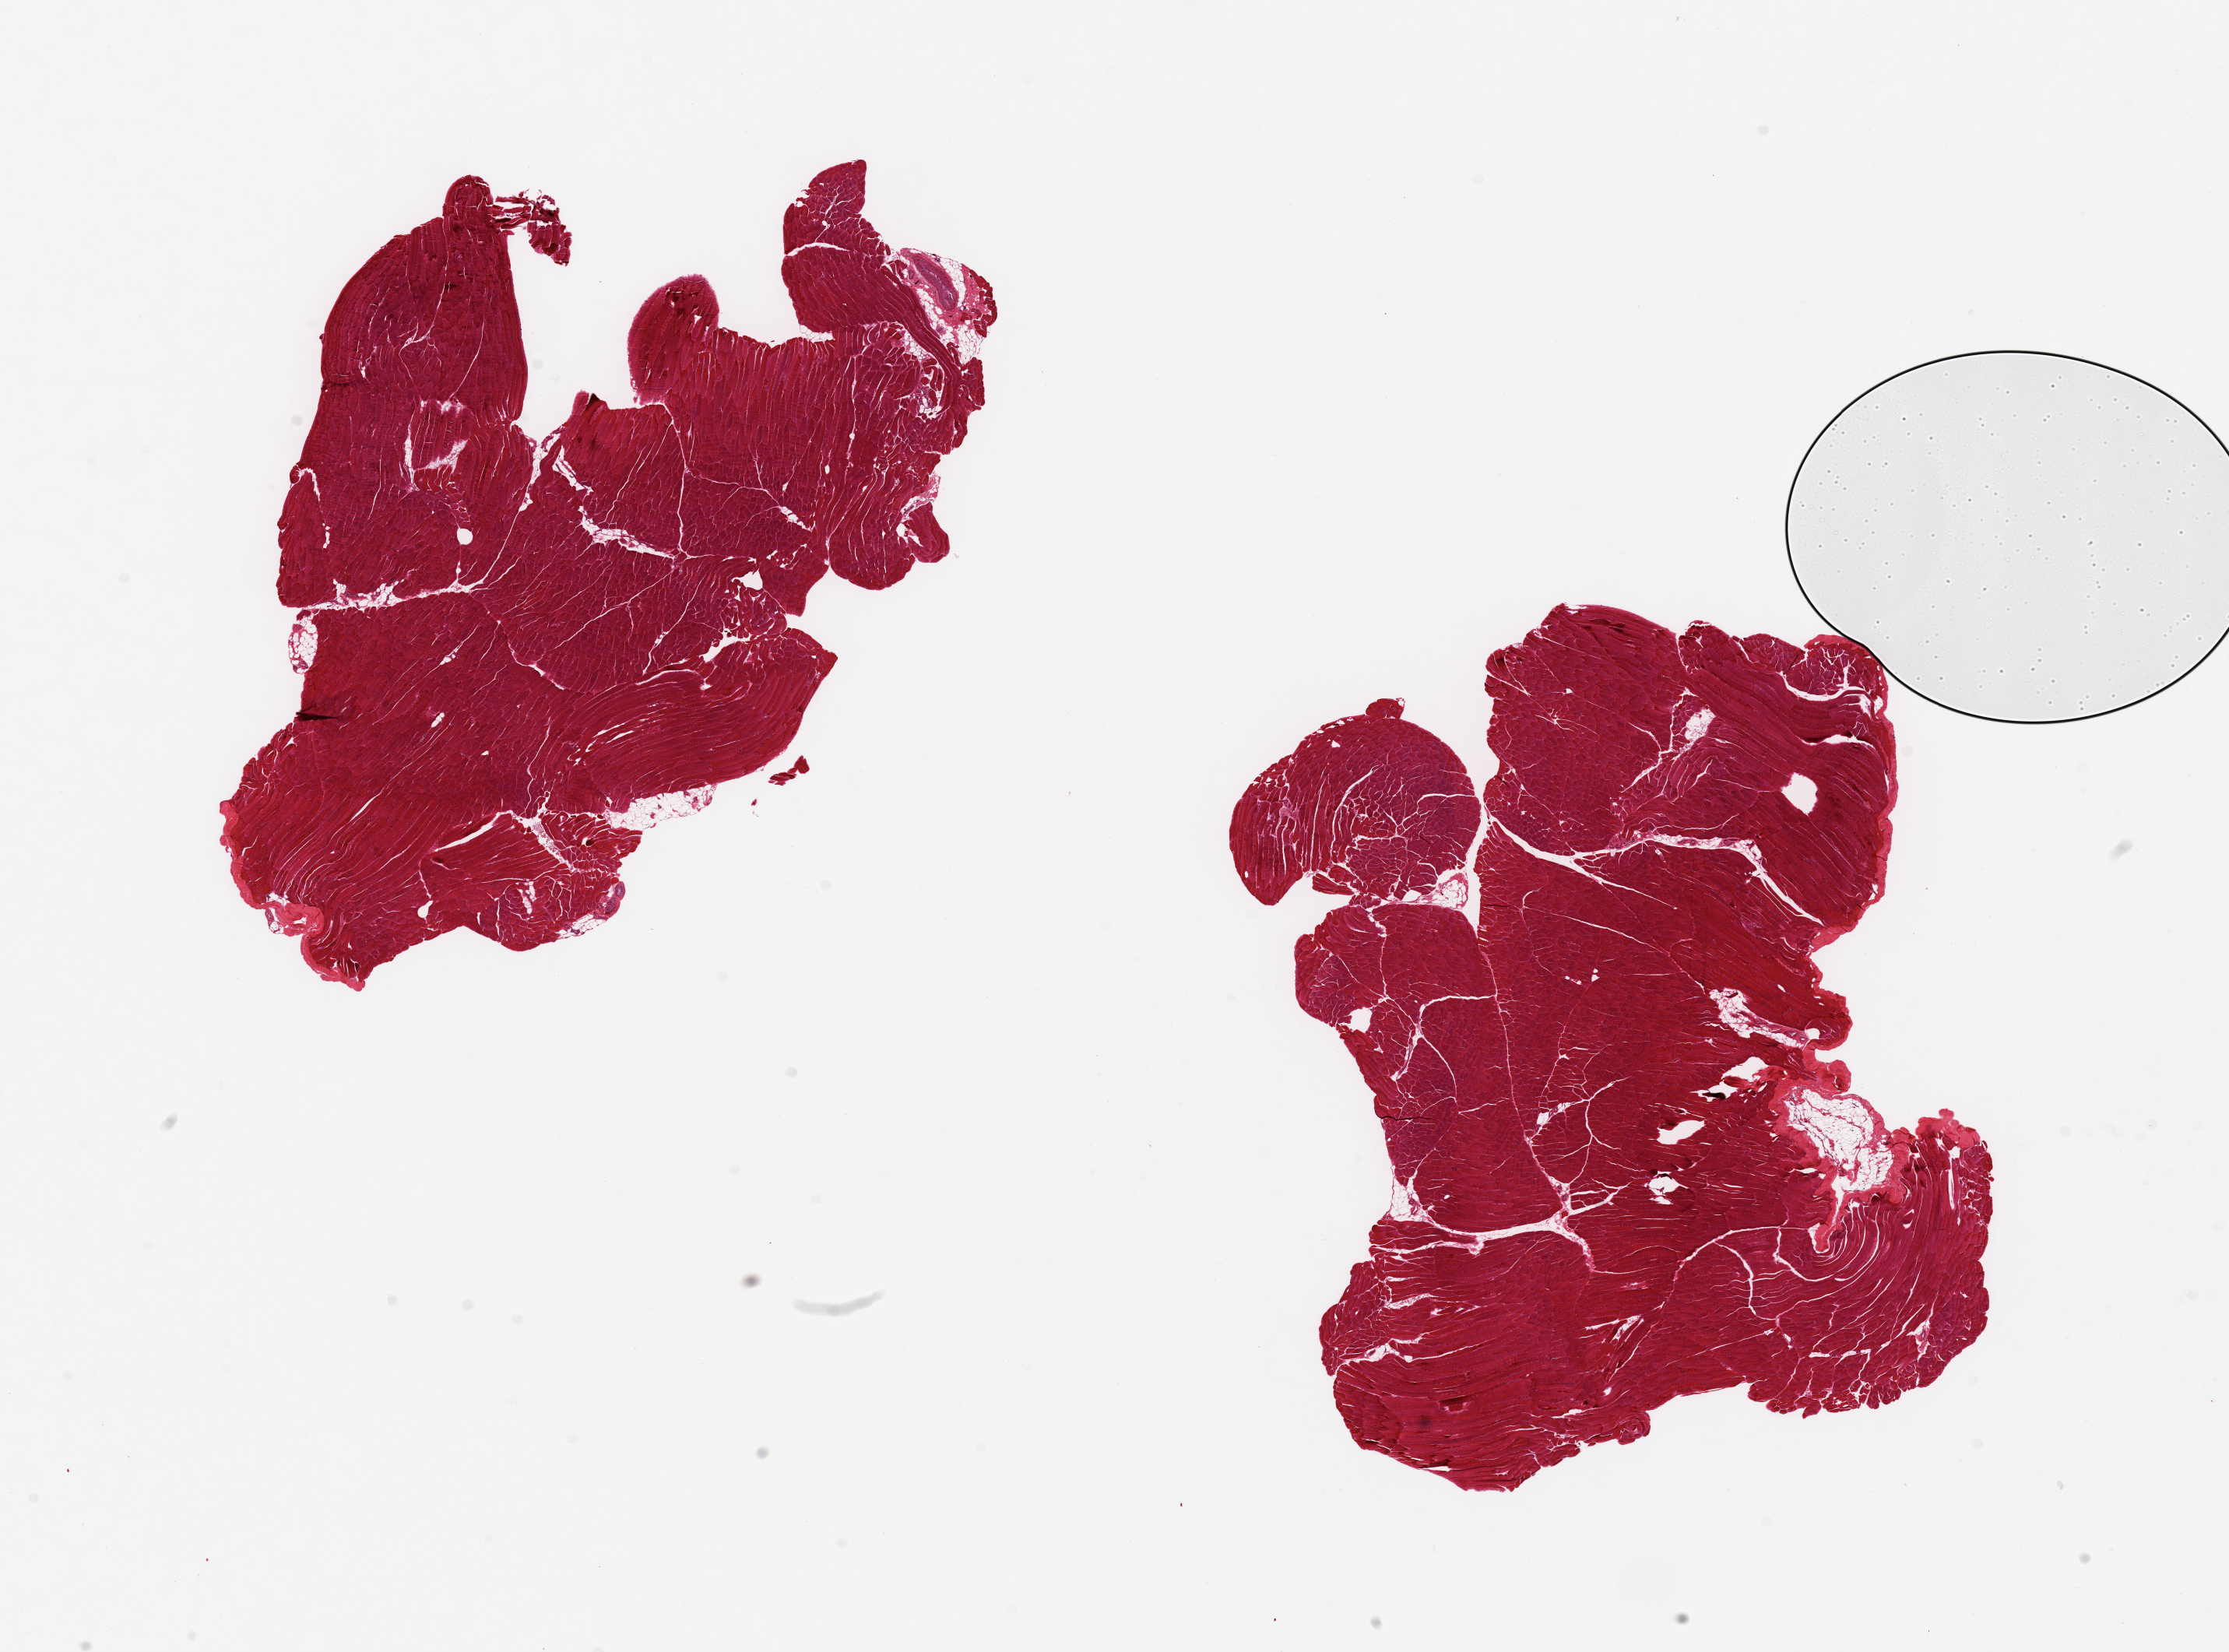
Whole-slide image, haematoxylin and eosin stain, brightfield, shown as a low-resolution overview of the whole scanned area (about 22.6 x 16.8 mm, from a 20x scan); PAXgene-fixed, paraffin-embedded tissue; target tissue: skeletal muscle; donor tissue sample. Donor: female.
Pathologist's review note for this sample: 2 pieces, 10x7 & 9x7mm; no extraneous tissue.